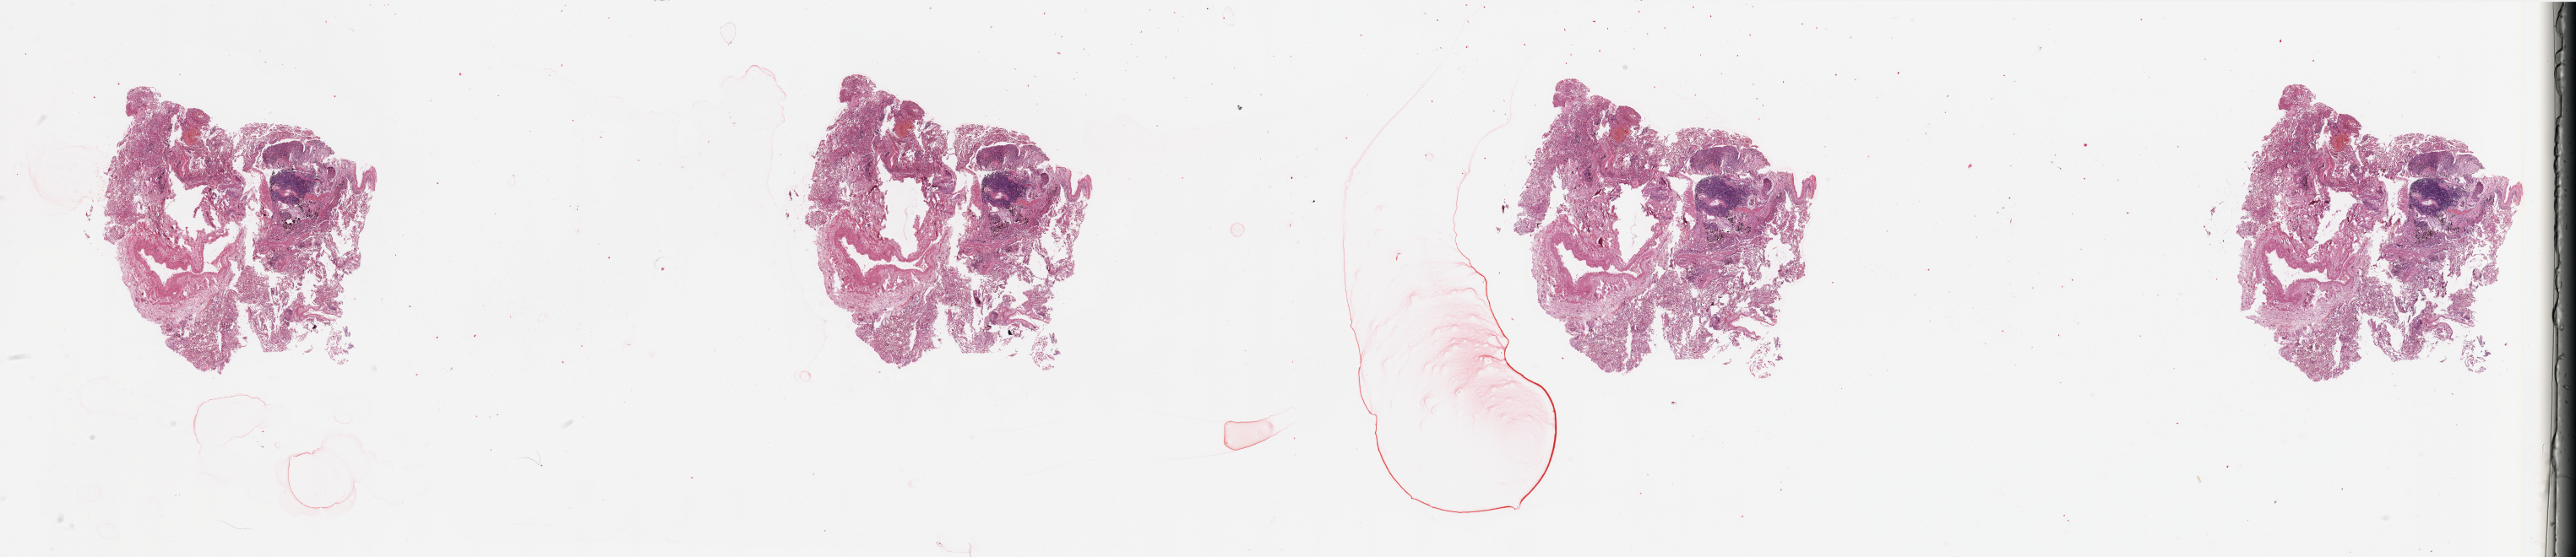
H&E-stained whole-slide image, a low-resolution overview of the entire scanned area, about 48.2 x 10.4 mm (slide scanned at 20x). Normal (non-tumour) tissue sample, sampled site: lung. Male, 73 y/o.
This section: normal (non-tumour) tissue from the same patient. Patient diagnosis: Squamous cell carcinoma, NOS.